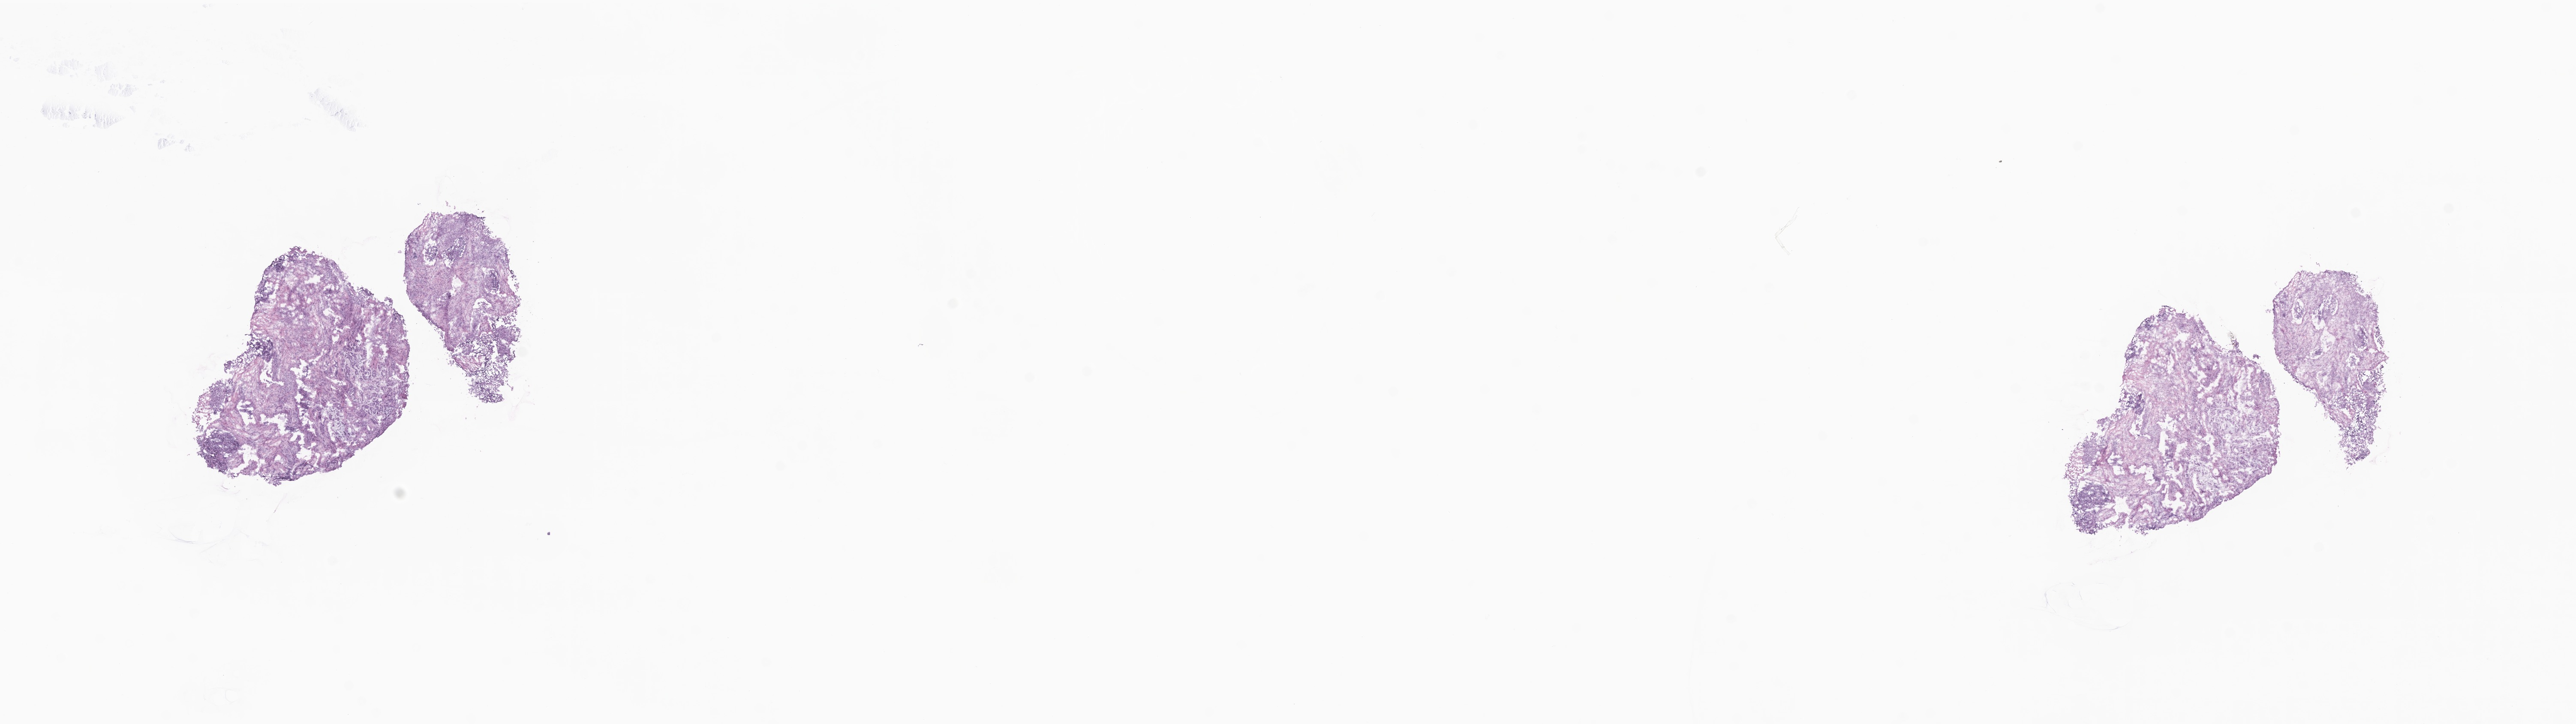
Hematoxylin and eosin (H&E) whole-slide image, whole scanned area (about 25.3 x 7.1 mm) shown as a low-resolution overview; frozen section; specimen: primary tumor; anatomic site: breast (left). Female, age 54 years at initial diagnosis. Pathologist review of this section (percent, as recorded): tumor cells 47%, tumor nuclei 75%, stromal cells 51%, necrosis 2%, normal cells 0%. Inflammatory infiltration, as recorded: lymphocyte infiltration 14%, monocyte infiltration 1%, neutrophil infiltration 0%.
• diagnosis: Infiltrating duct carcinoma, NOS
• section: top of the tissue portion